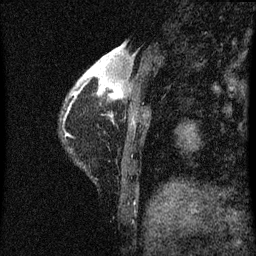
Breast MRI (dynamic contrast-enhanced), one sagittal slice. Slice 12 of 60 in the series (ordered by position). Dynamic contrast-enhanced series, image 2 of 3 at this slice position (ordered by acquisition). 1.5 T. TE 4.2 ms, TR 8 ms. 256 × 256 image matrix, field of view 180 × 180 mm. Female patient, age 38 years.
Outlined on this slice (semi-automatic segmentation, software-assisted and operator-edited):
- analysis volume of interest (the breast-tissue region the enhancement analysis was run in; not a lesion): box from (x=67, y=44) to (x=142, y=125) px
- tumour enhancement mask (voxels above the 70 % enhancement threshold inside the analysis volume of interest): (x=101, y=46)–(x=123, y=97)